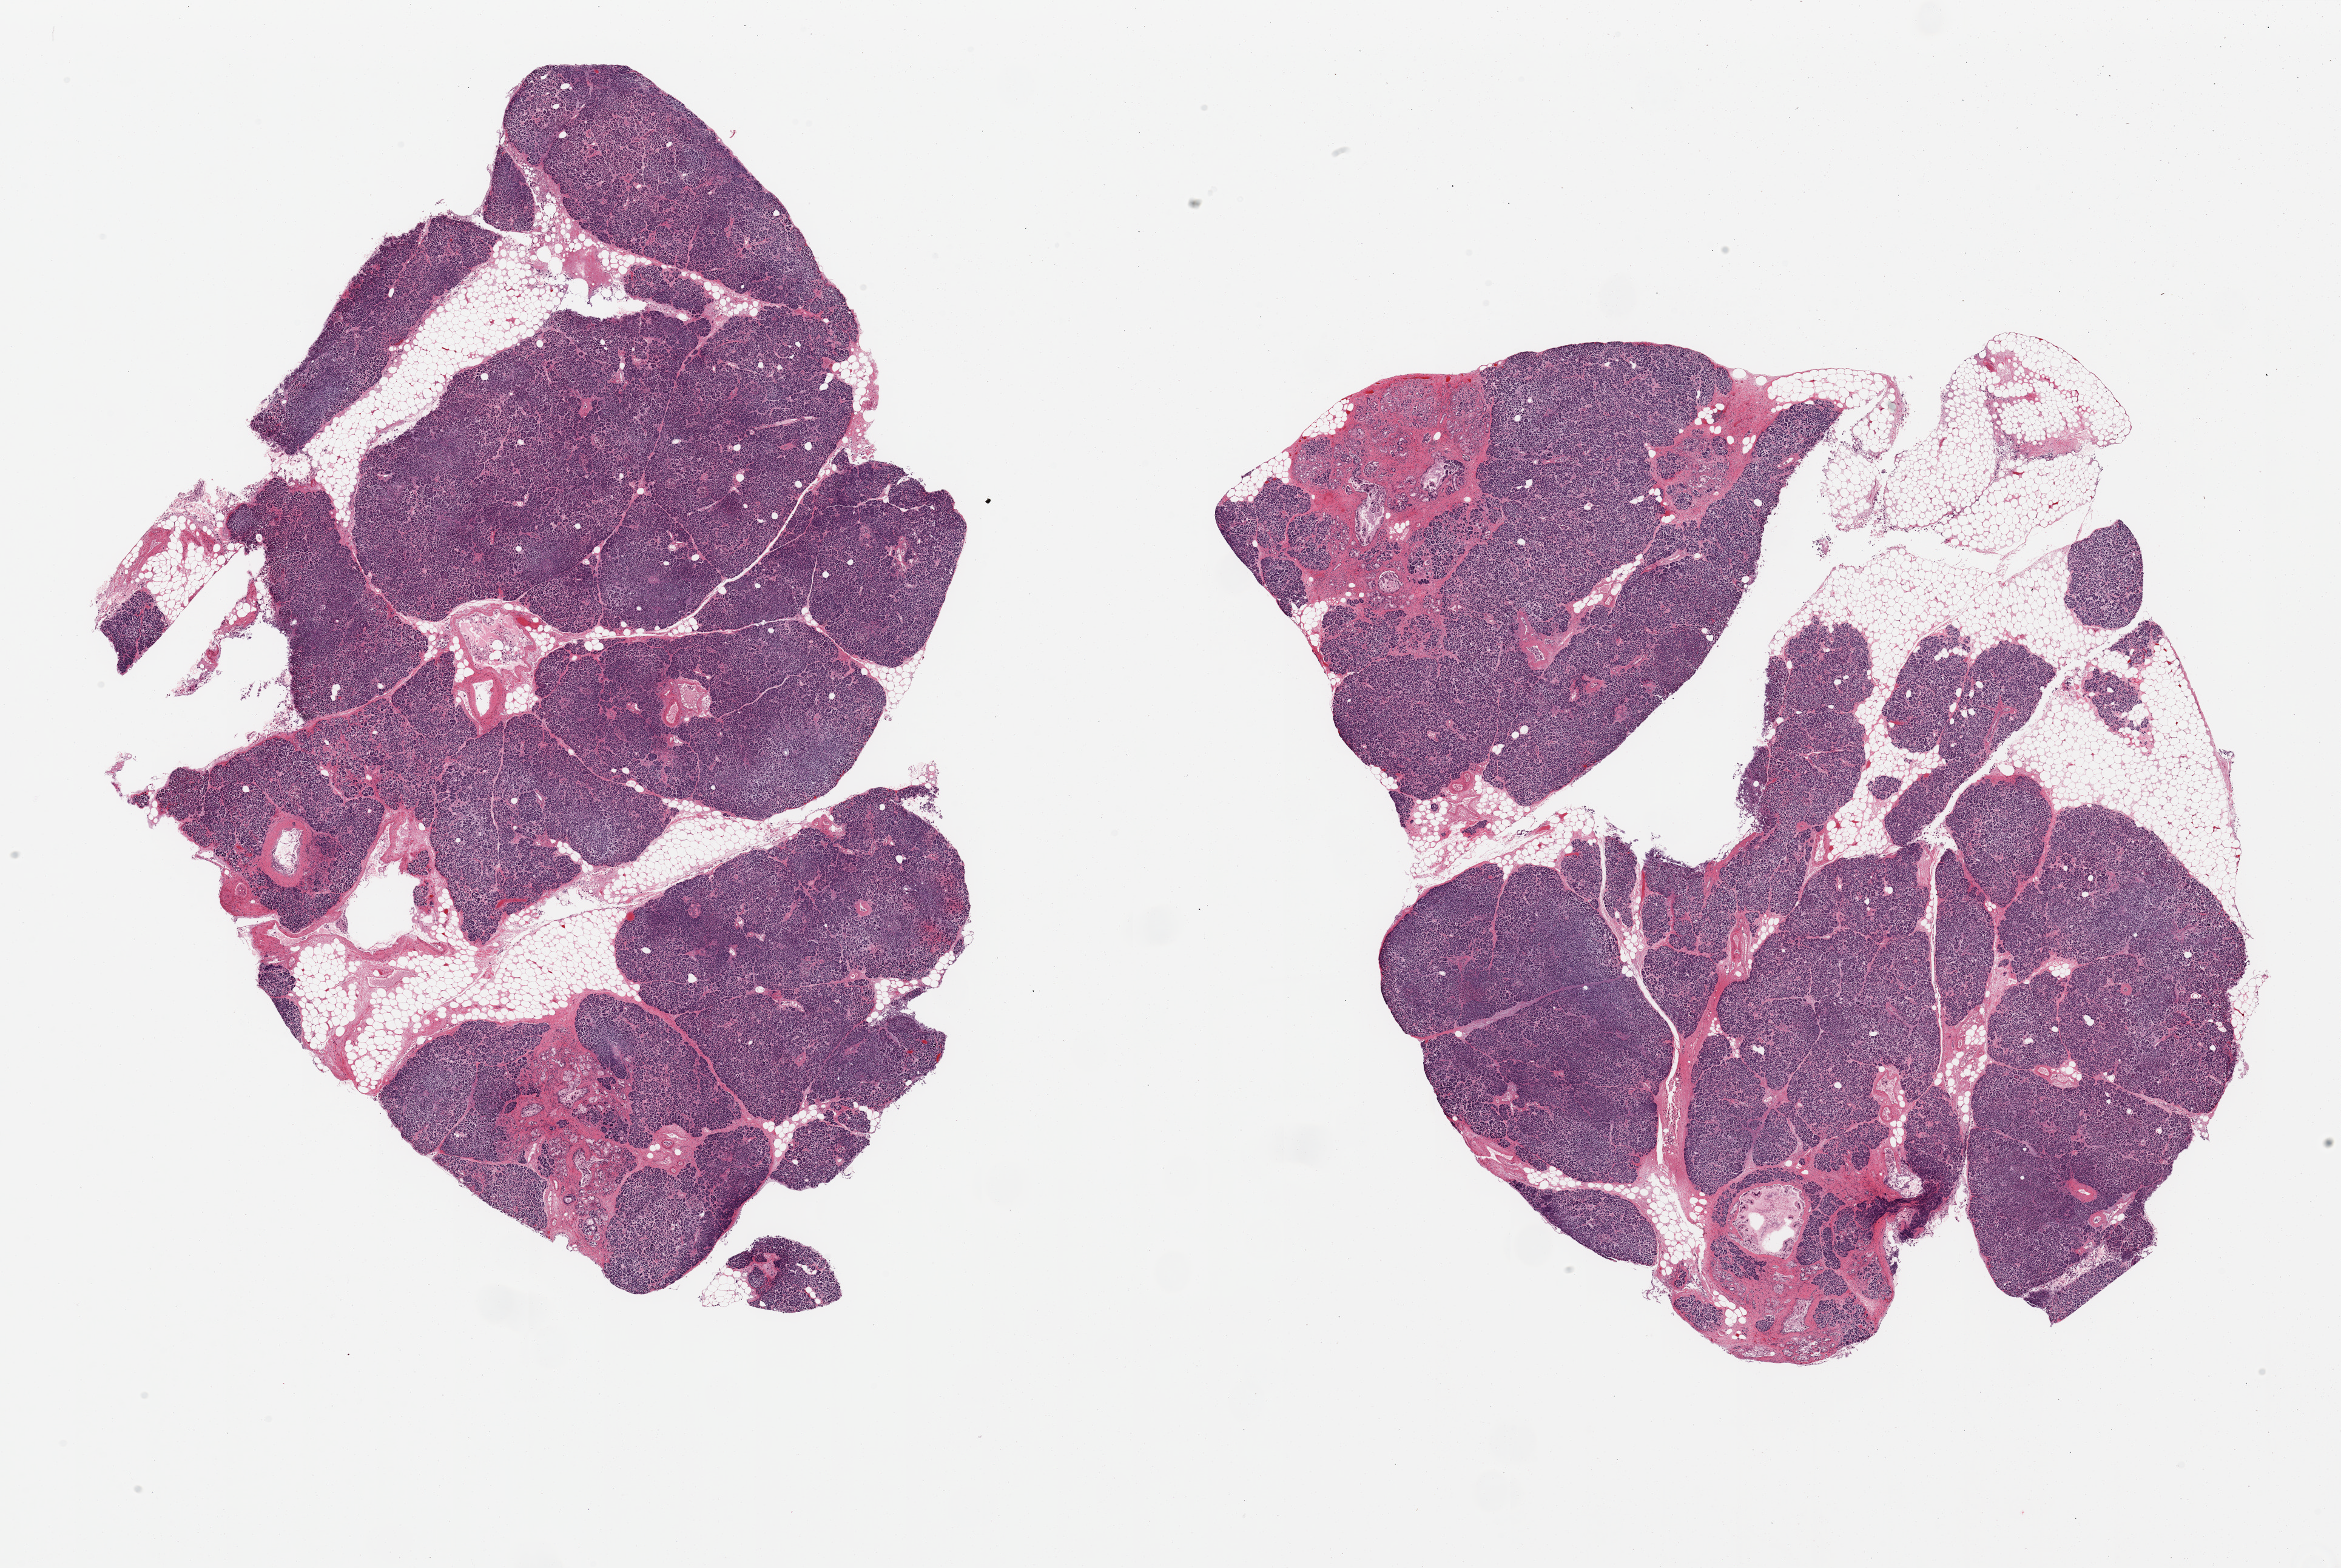
Haematoxylin and eosin whole-slide image — low-resolution overview of the scanned area, about 30.5 x 20.4 mm (from a 20x scan); PAXgene-fixed paraffin-embedded (PFPE) section; target tissue: pancreas; donor tissue sample. Donor: male.
- pathologist's review note for this sample: 2 pieces; 20% internal fat